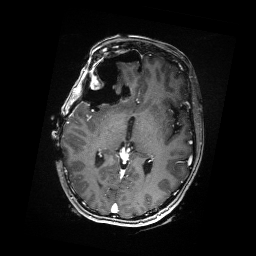
Brain MRI from a brain-tumour surgery series, one axial slice; slice 94 of 176 in the series (ordered by position); T1-weighted post-contrast; 256 × 256 image matrix. From the clinical record (not read from this slice): histopathology: Metastatic Carcinoma from Breast primary; tumour location: Right Frontal.
Structures marked on this image (expert manual segmentation):
- residual tumour: bounding box [x1, y1, x2, y2] px = [91, 68, 105, 87]